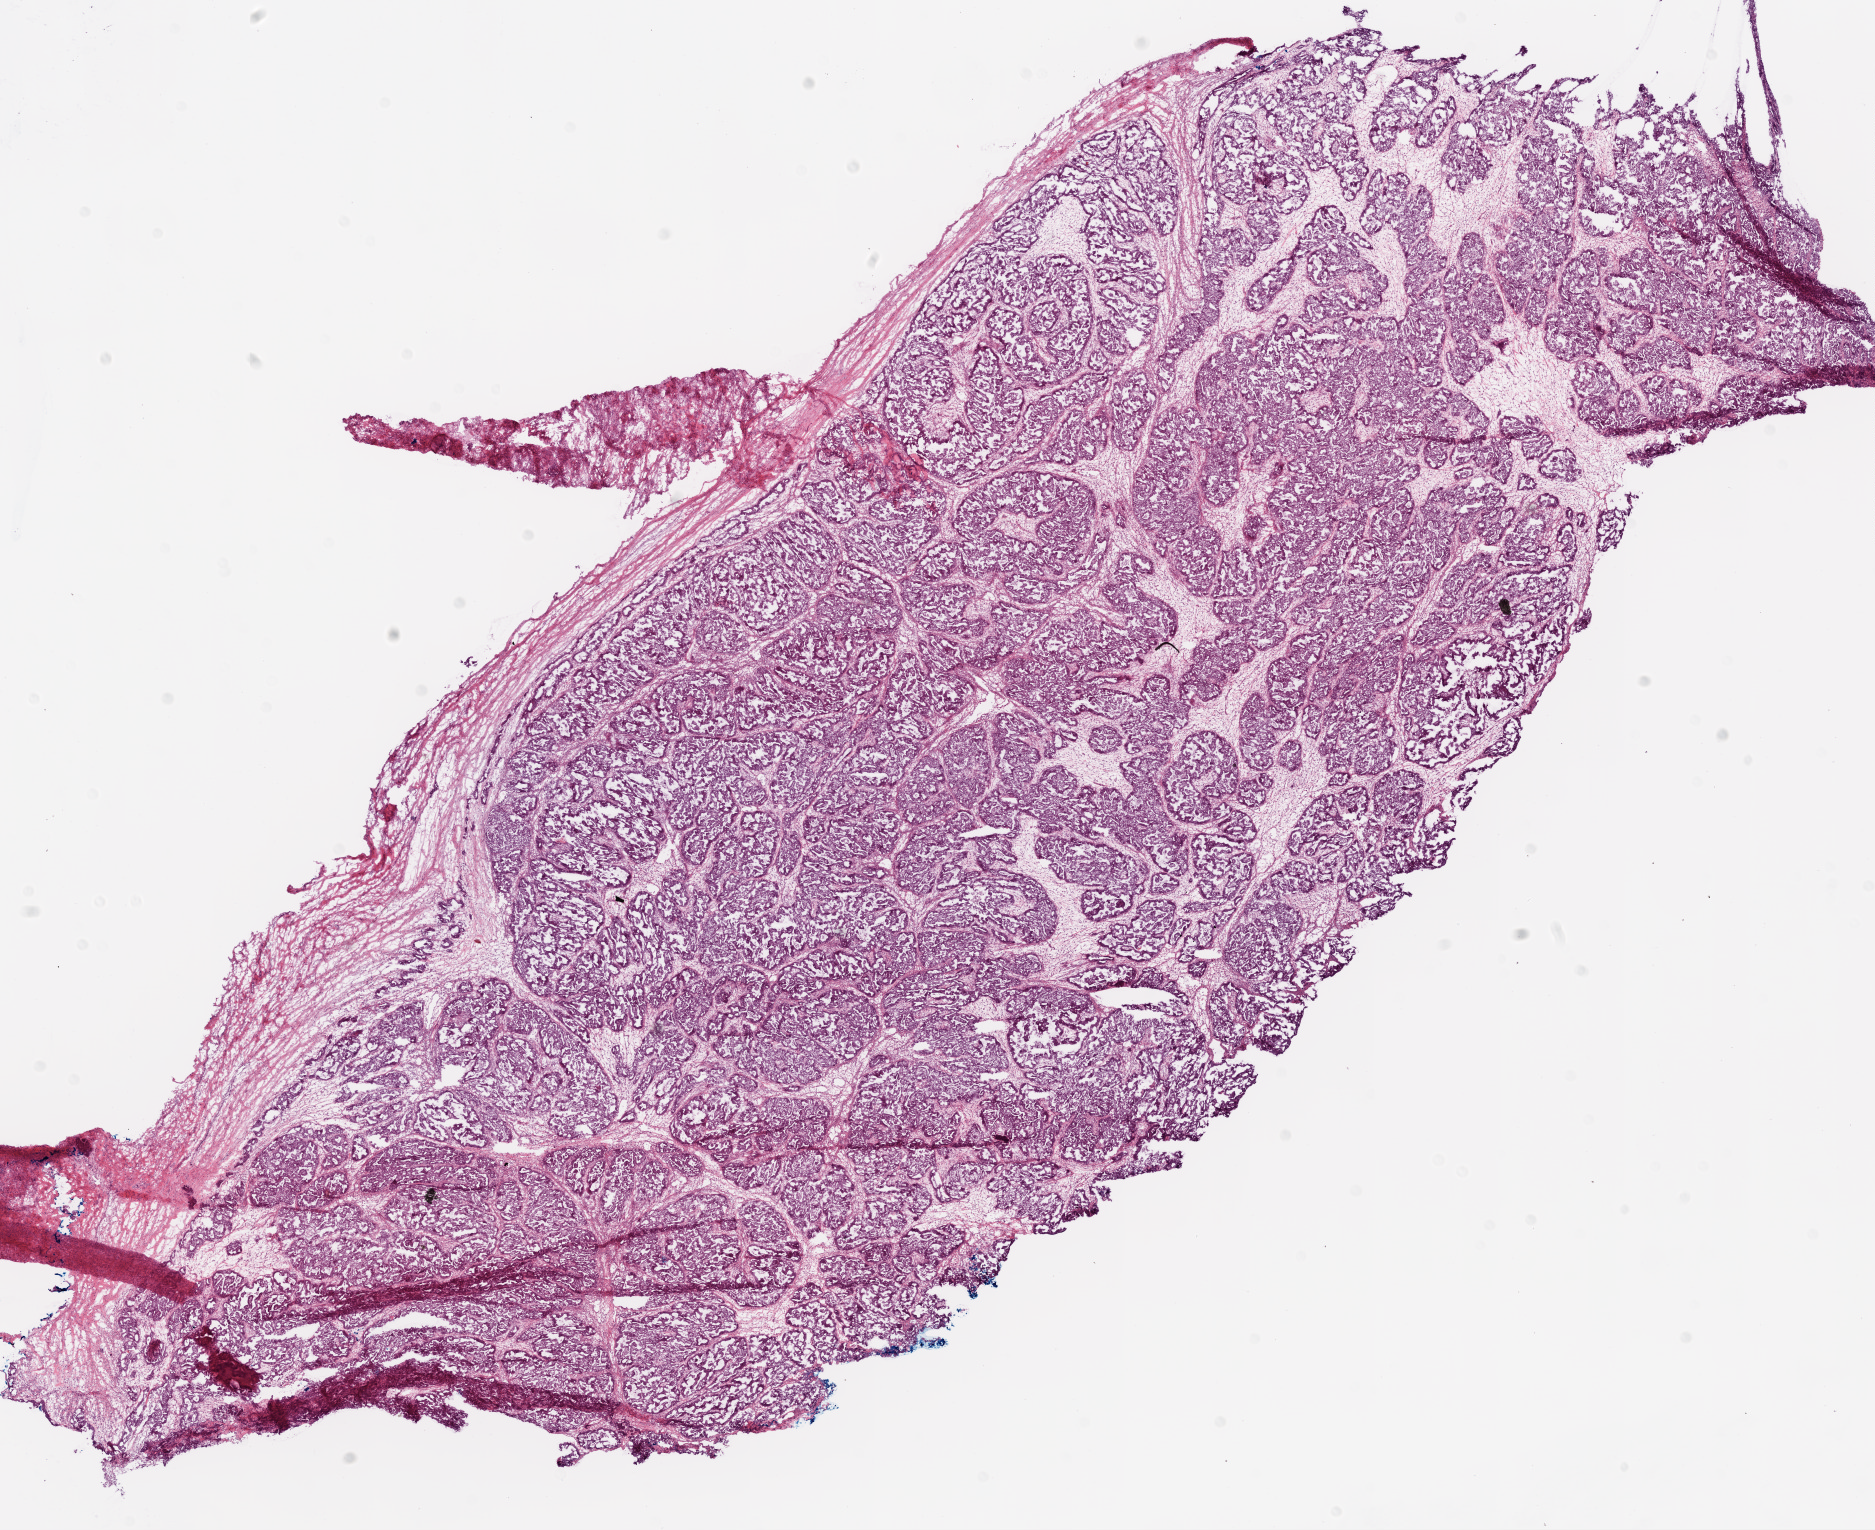
H&E-stained whole-slide image, low-resolution overview of the scanned area, about 15.0 x 12.3 mm; frozen section from the bottom of the tissue portion; primary tumour sample from the ovary. Female, age 47 years at initial diagnosis. Histologic grade: G3 (poorly differentiated). Composition of this section per pathologist review: tumour cells 90%, tumour nuclei 90%, normal cells 0%, stromal cells 10%, necrosis 0%.
FIGO stage: IIIC. Laterality: bilateral. Histologic diagnosis: Serous cystadenocarcinoma, NOS.